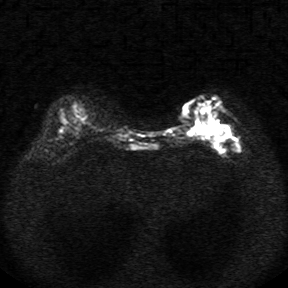
Breast MRI, one axial slice; slice 11 of 34 in the series (ordered by position); diffusion-weighted series; image 2 of 4 stored at this slice position (different b-values; order by instance number); 1.5 T; 5 mm slice thickness; 288 × 288 image matrix. Female patient.
Structures marked on this image (outlined manually by an expert reader):
- tumour on diffusion-weighted imaging: bounding box [x1, y1, x2, y2] px = [190, 125, 204, 135]